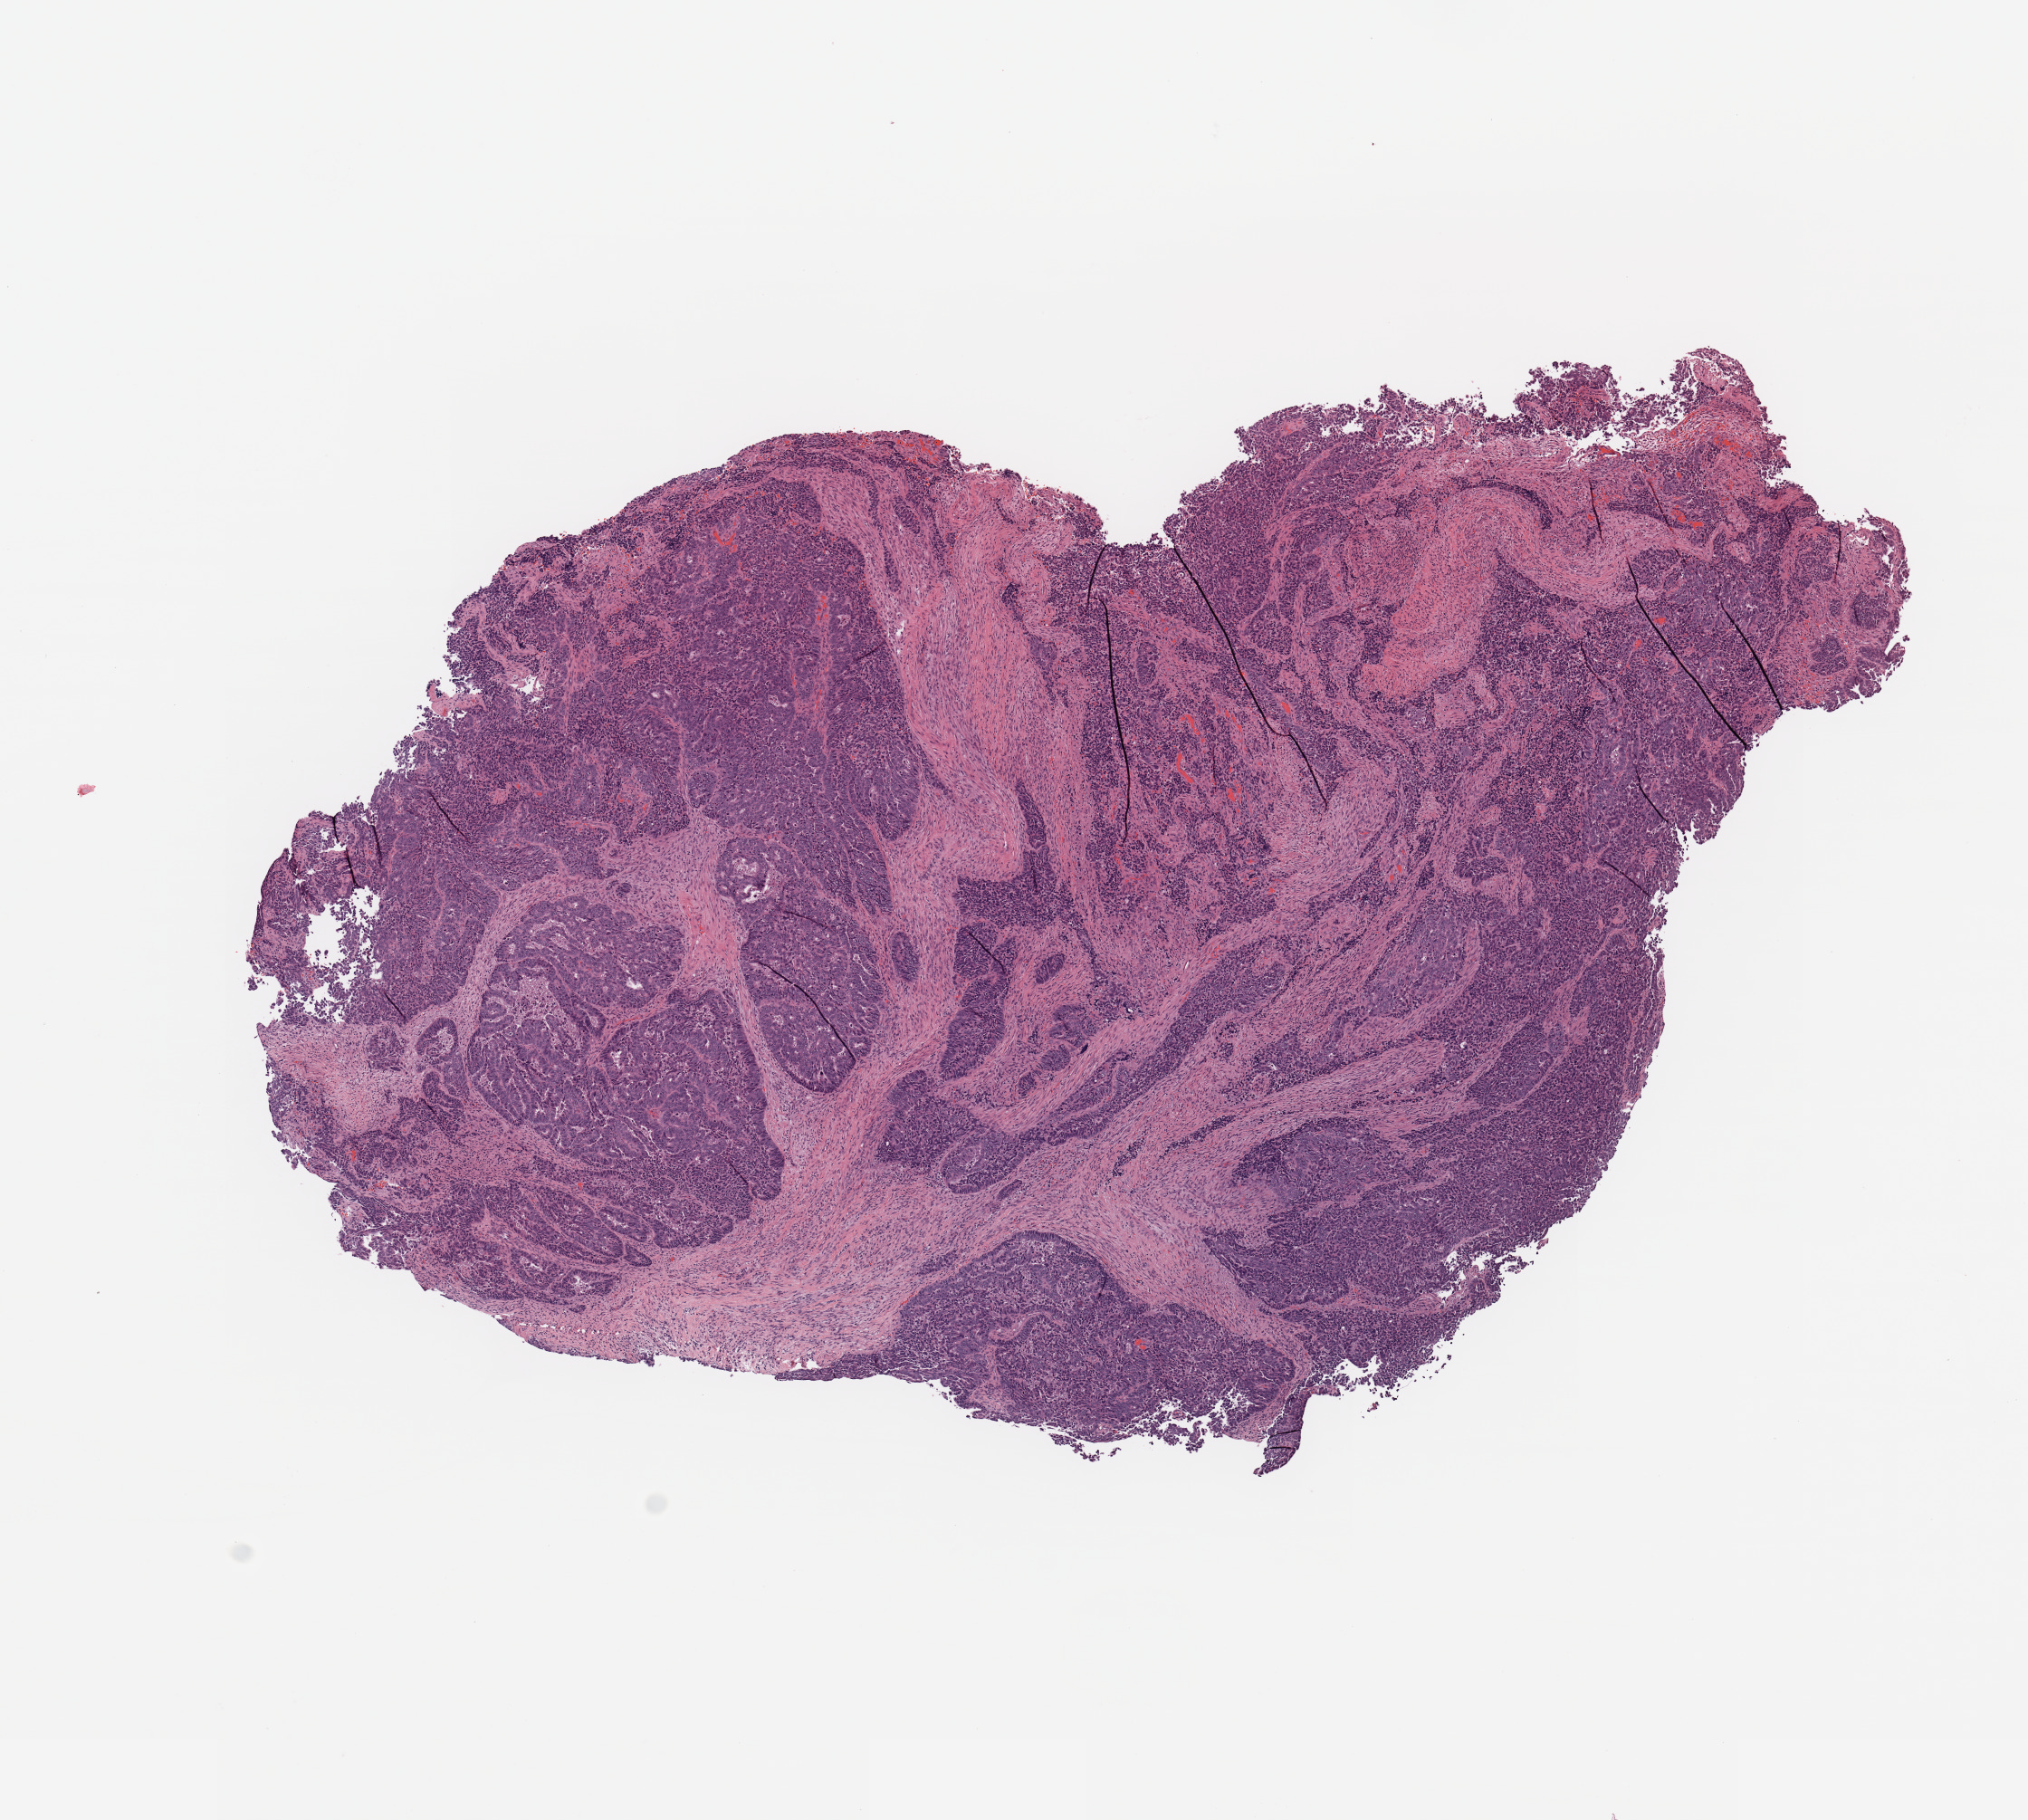
H&E-stained whole-slide image — low-resolution overview of the scanned area, about 8.9 x 7.9 mm; uterus, tumour tissue. 67-year-old female patient.
Histologic diagnosis: Endometrioid adenocarcinoma, NOS.